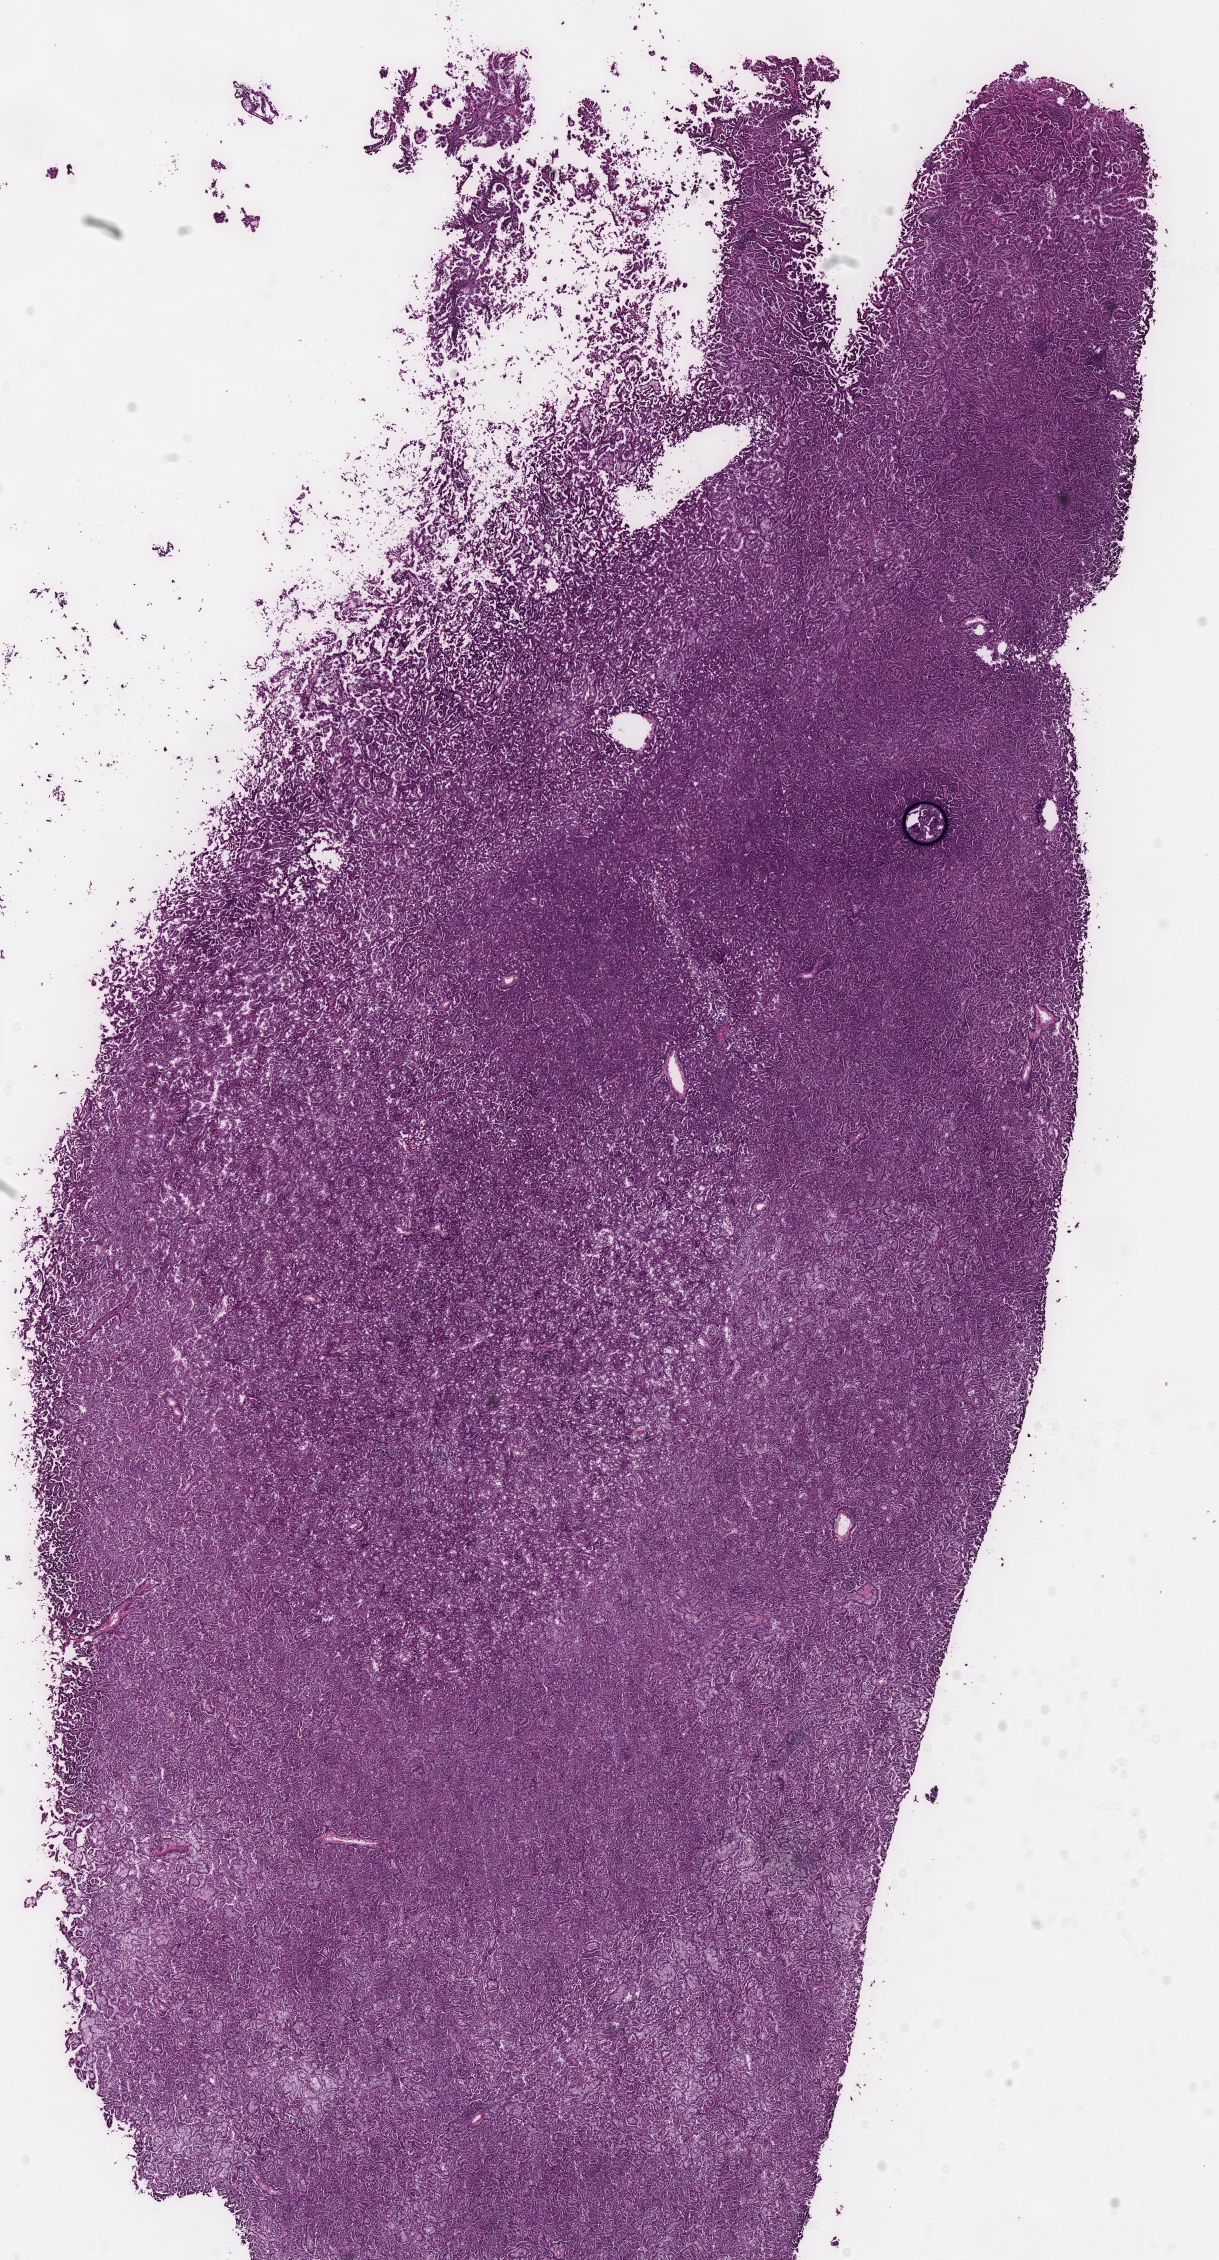
Whole-slide histology image, Hematoxylin and eosin (H&E) stained, whole scanned area (about 9.6 x 17.8 mm, acquisition: 40x scan) shown as a low-resolution overview, frozen section, kidney, primary tumour sample. Patient: male, age at initial diagnosis 61 years. Slide review estimates, as recorded: tumour cells 100%, tumour nuclei 80%.
Diagnosis: Papillary adenocarcinoma, NOS.